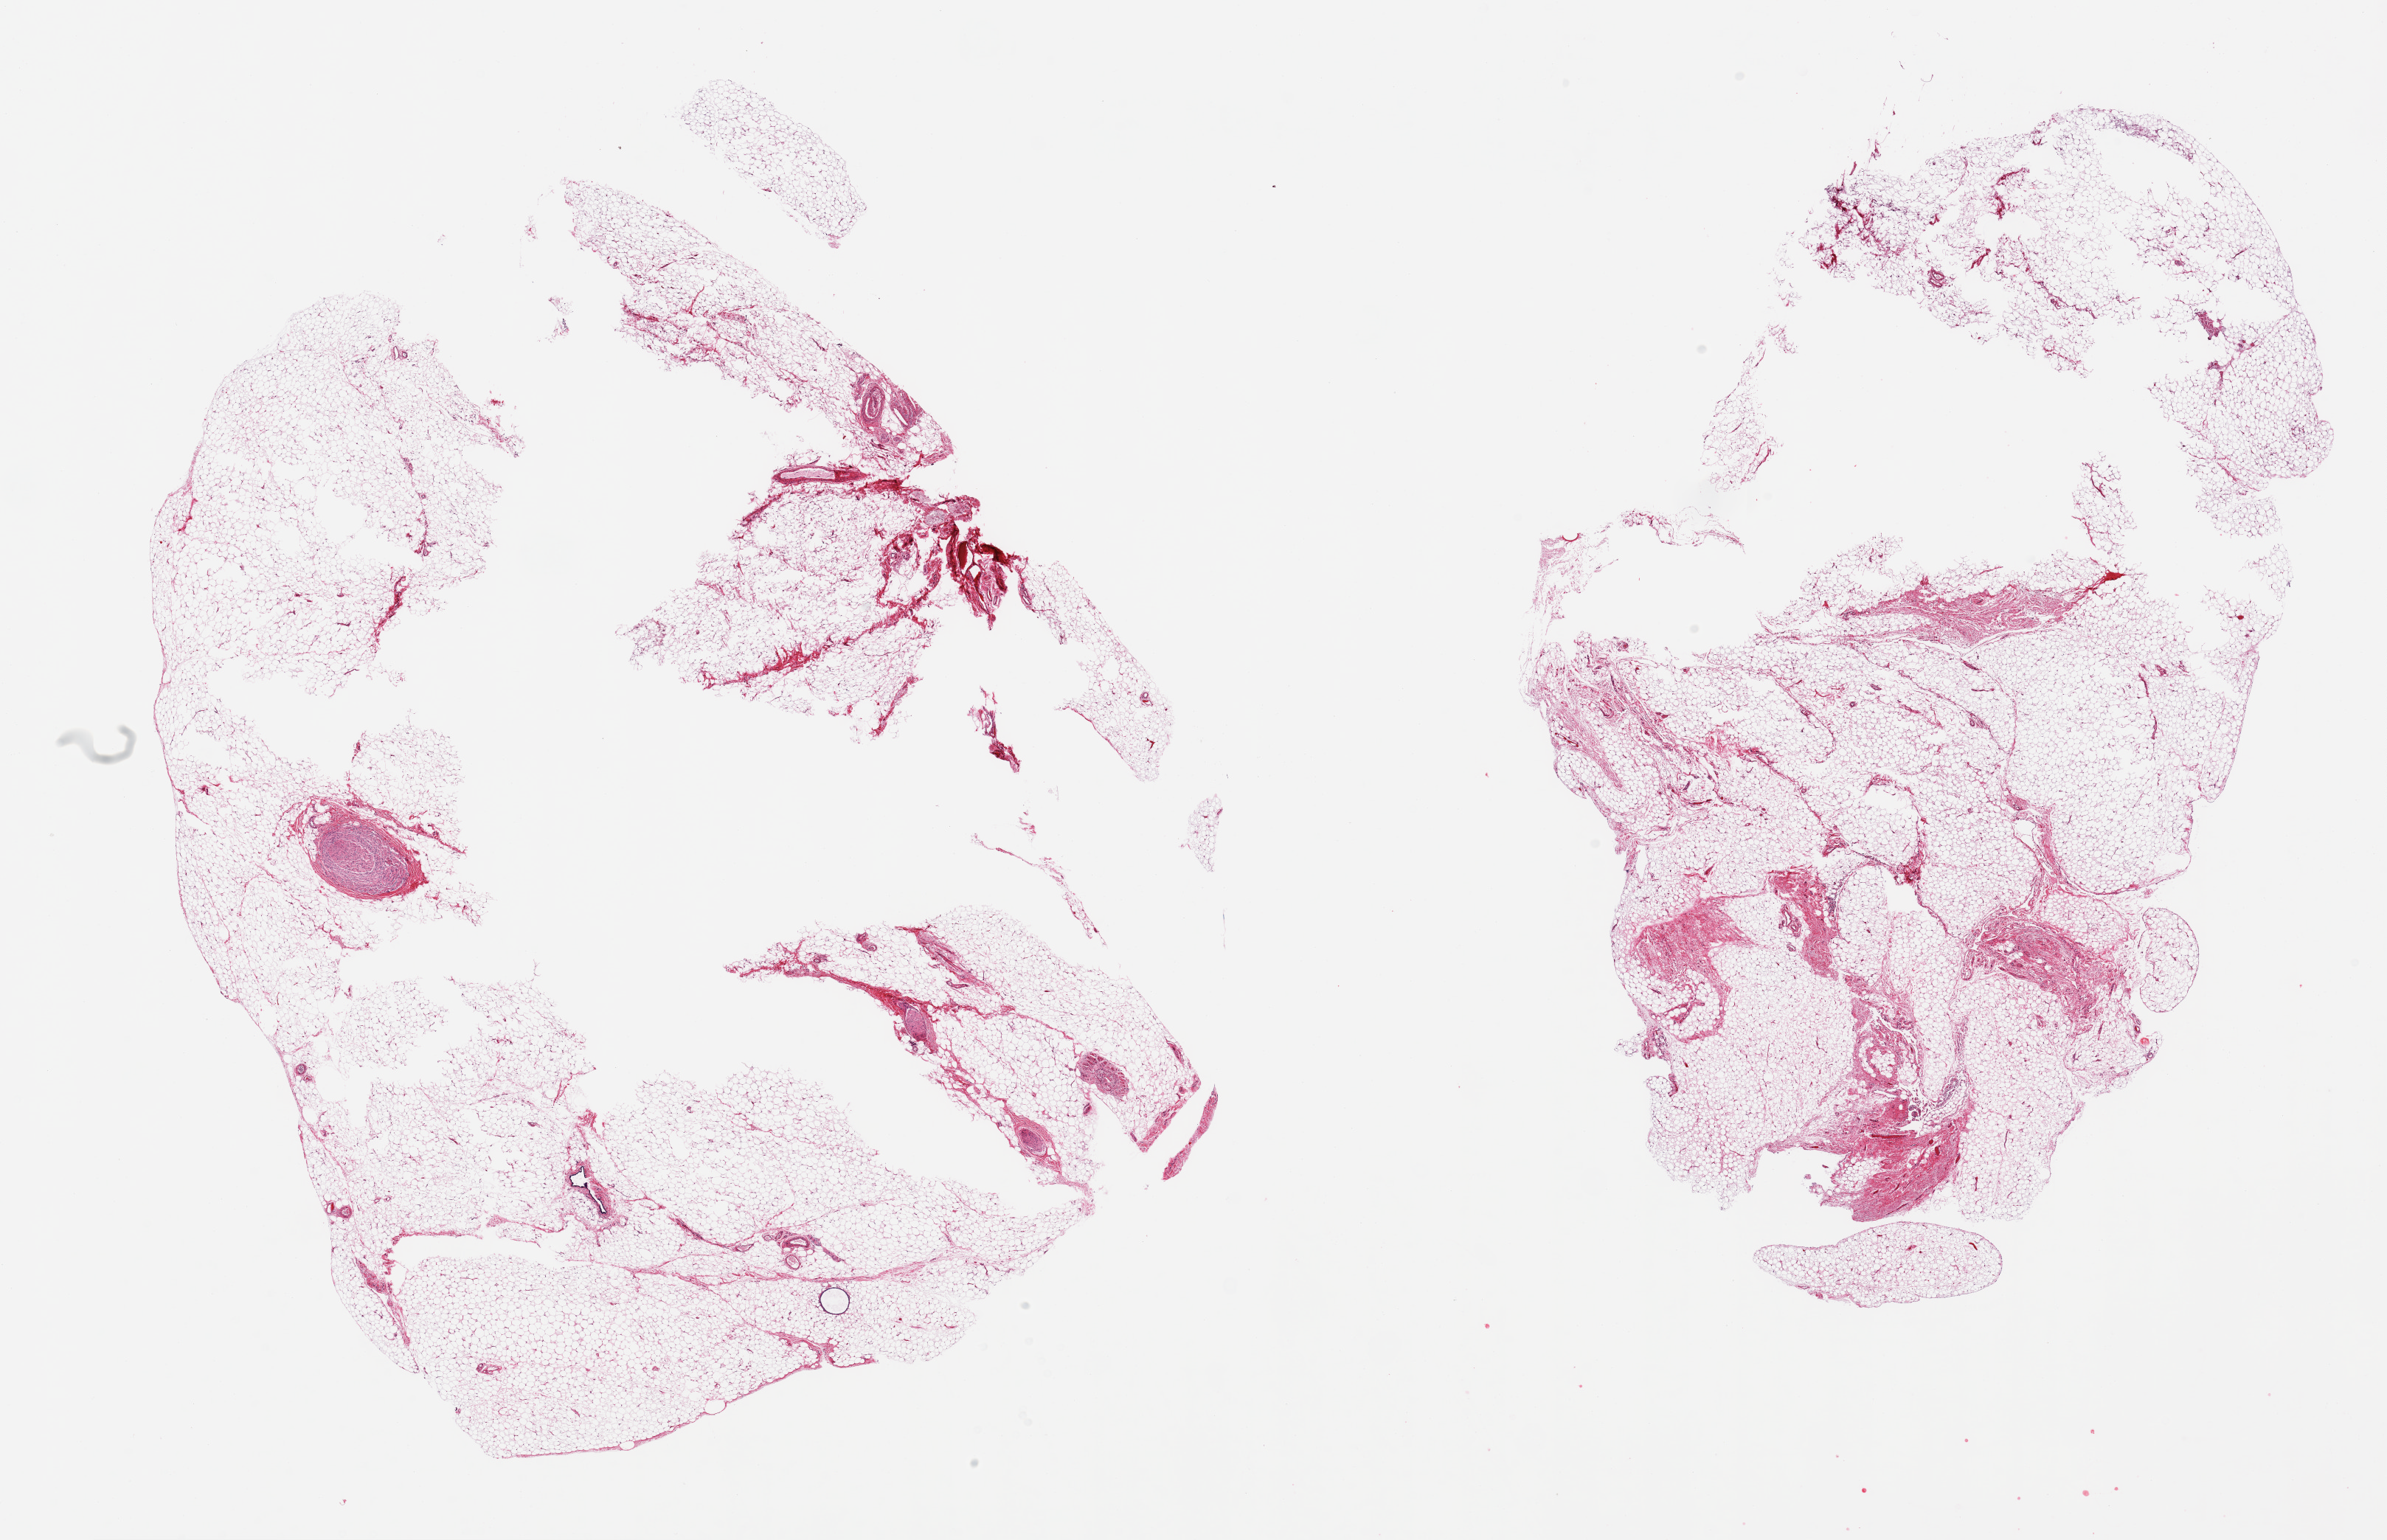
Digitized H&E-stained section, a low-resolution overview of the entire scanned area, about 25.6 x 16.5 mm. PAXgene-fixed, paraffin-embedded tissue. Target tissue: omentum. Tissue donor sample. Donor: female.
Pathologist's review note for this sample: 2 pieces; partly fragmented; 10% fibrous content.